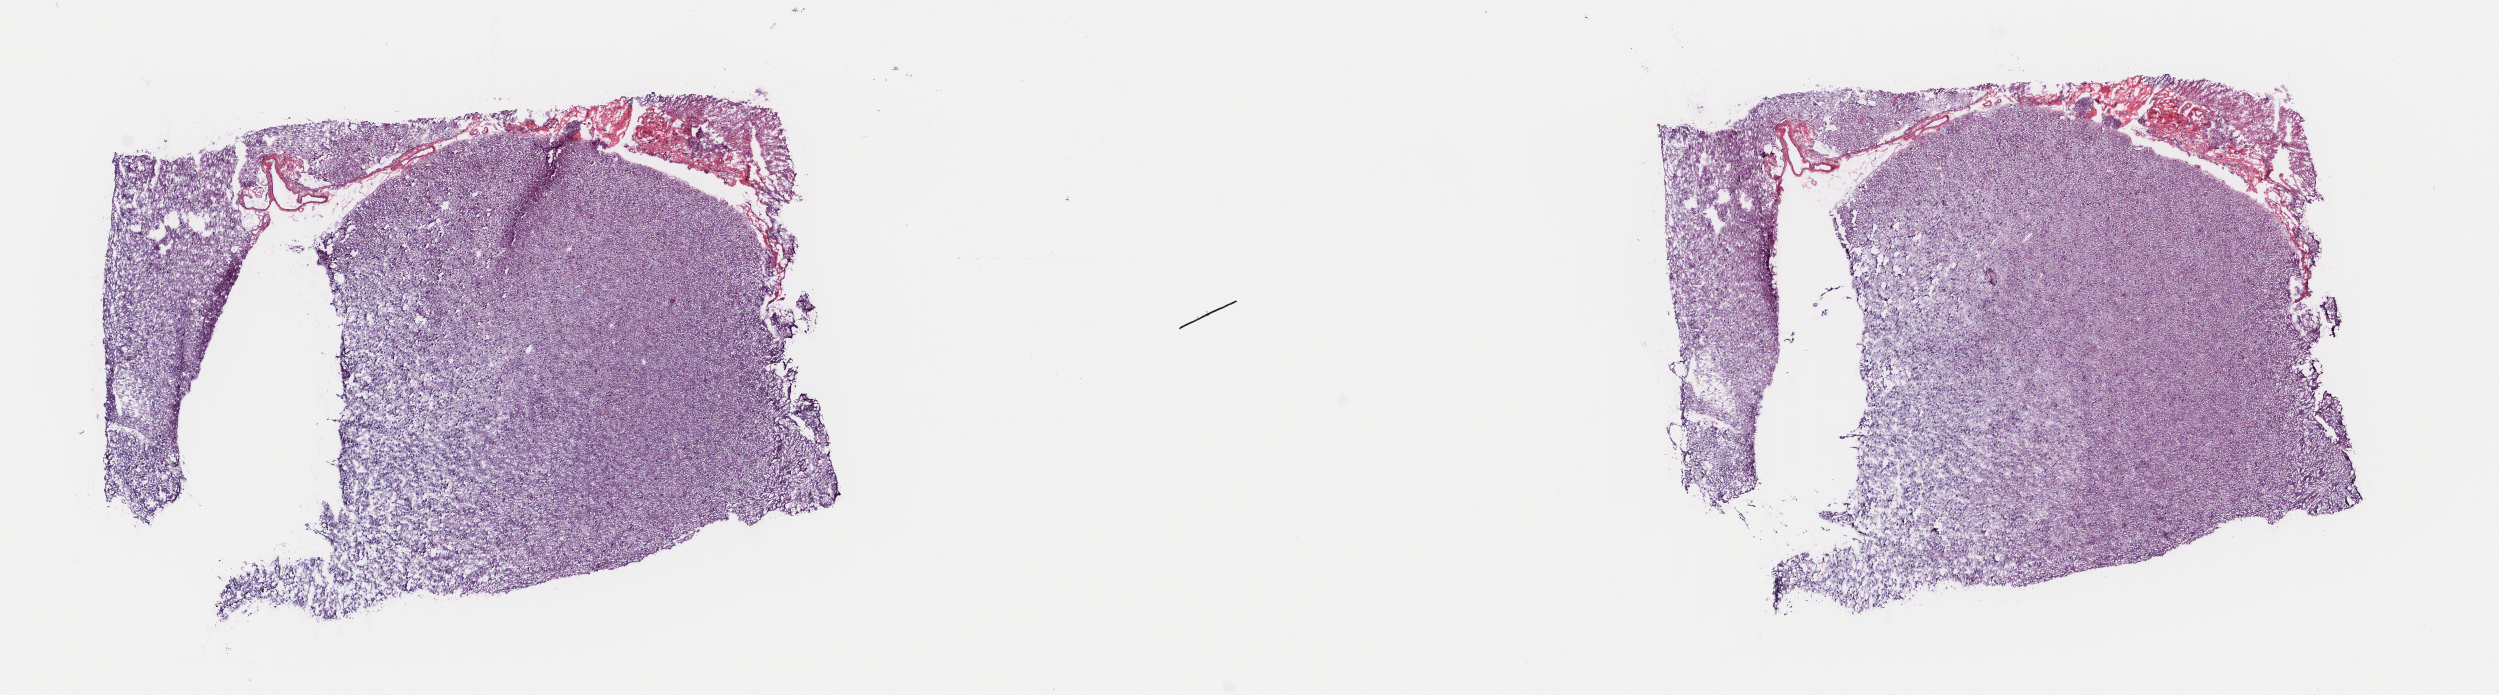
Whole-slide histology image, Hematoxylin and eosin (H&E) stained — whole scanned area (about 19.7 x 5.5 mm) shown as a low-resolution overview. Frozen section from the top of the tissue portion. Brain, primary tumour sample. Female patient; age at initial diagnosis 35 years. Pathologist review of this section (percent, as recorded): tumour cells 40%, tumour nuclei 70%.
Diagnosis: Mixed glioma (cerebrum).